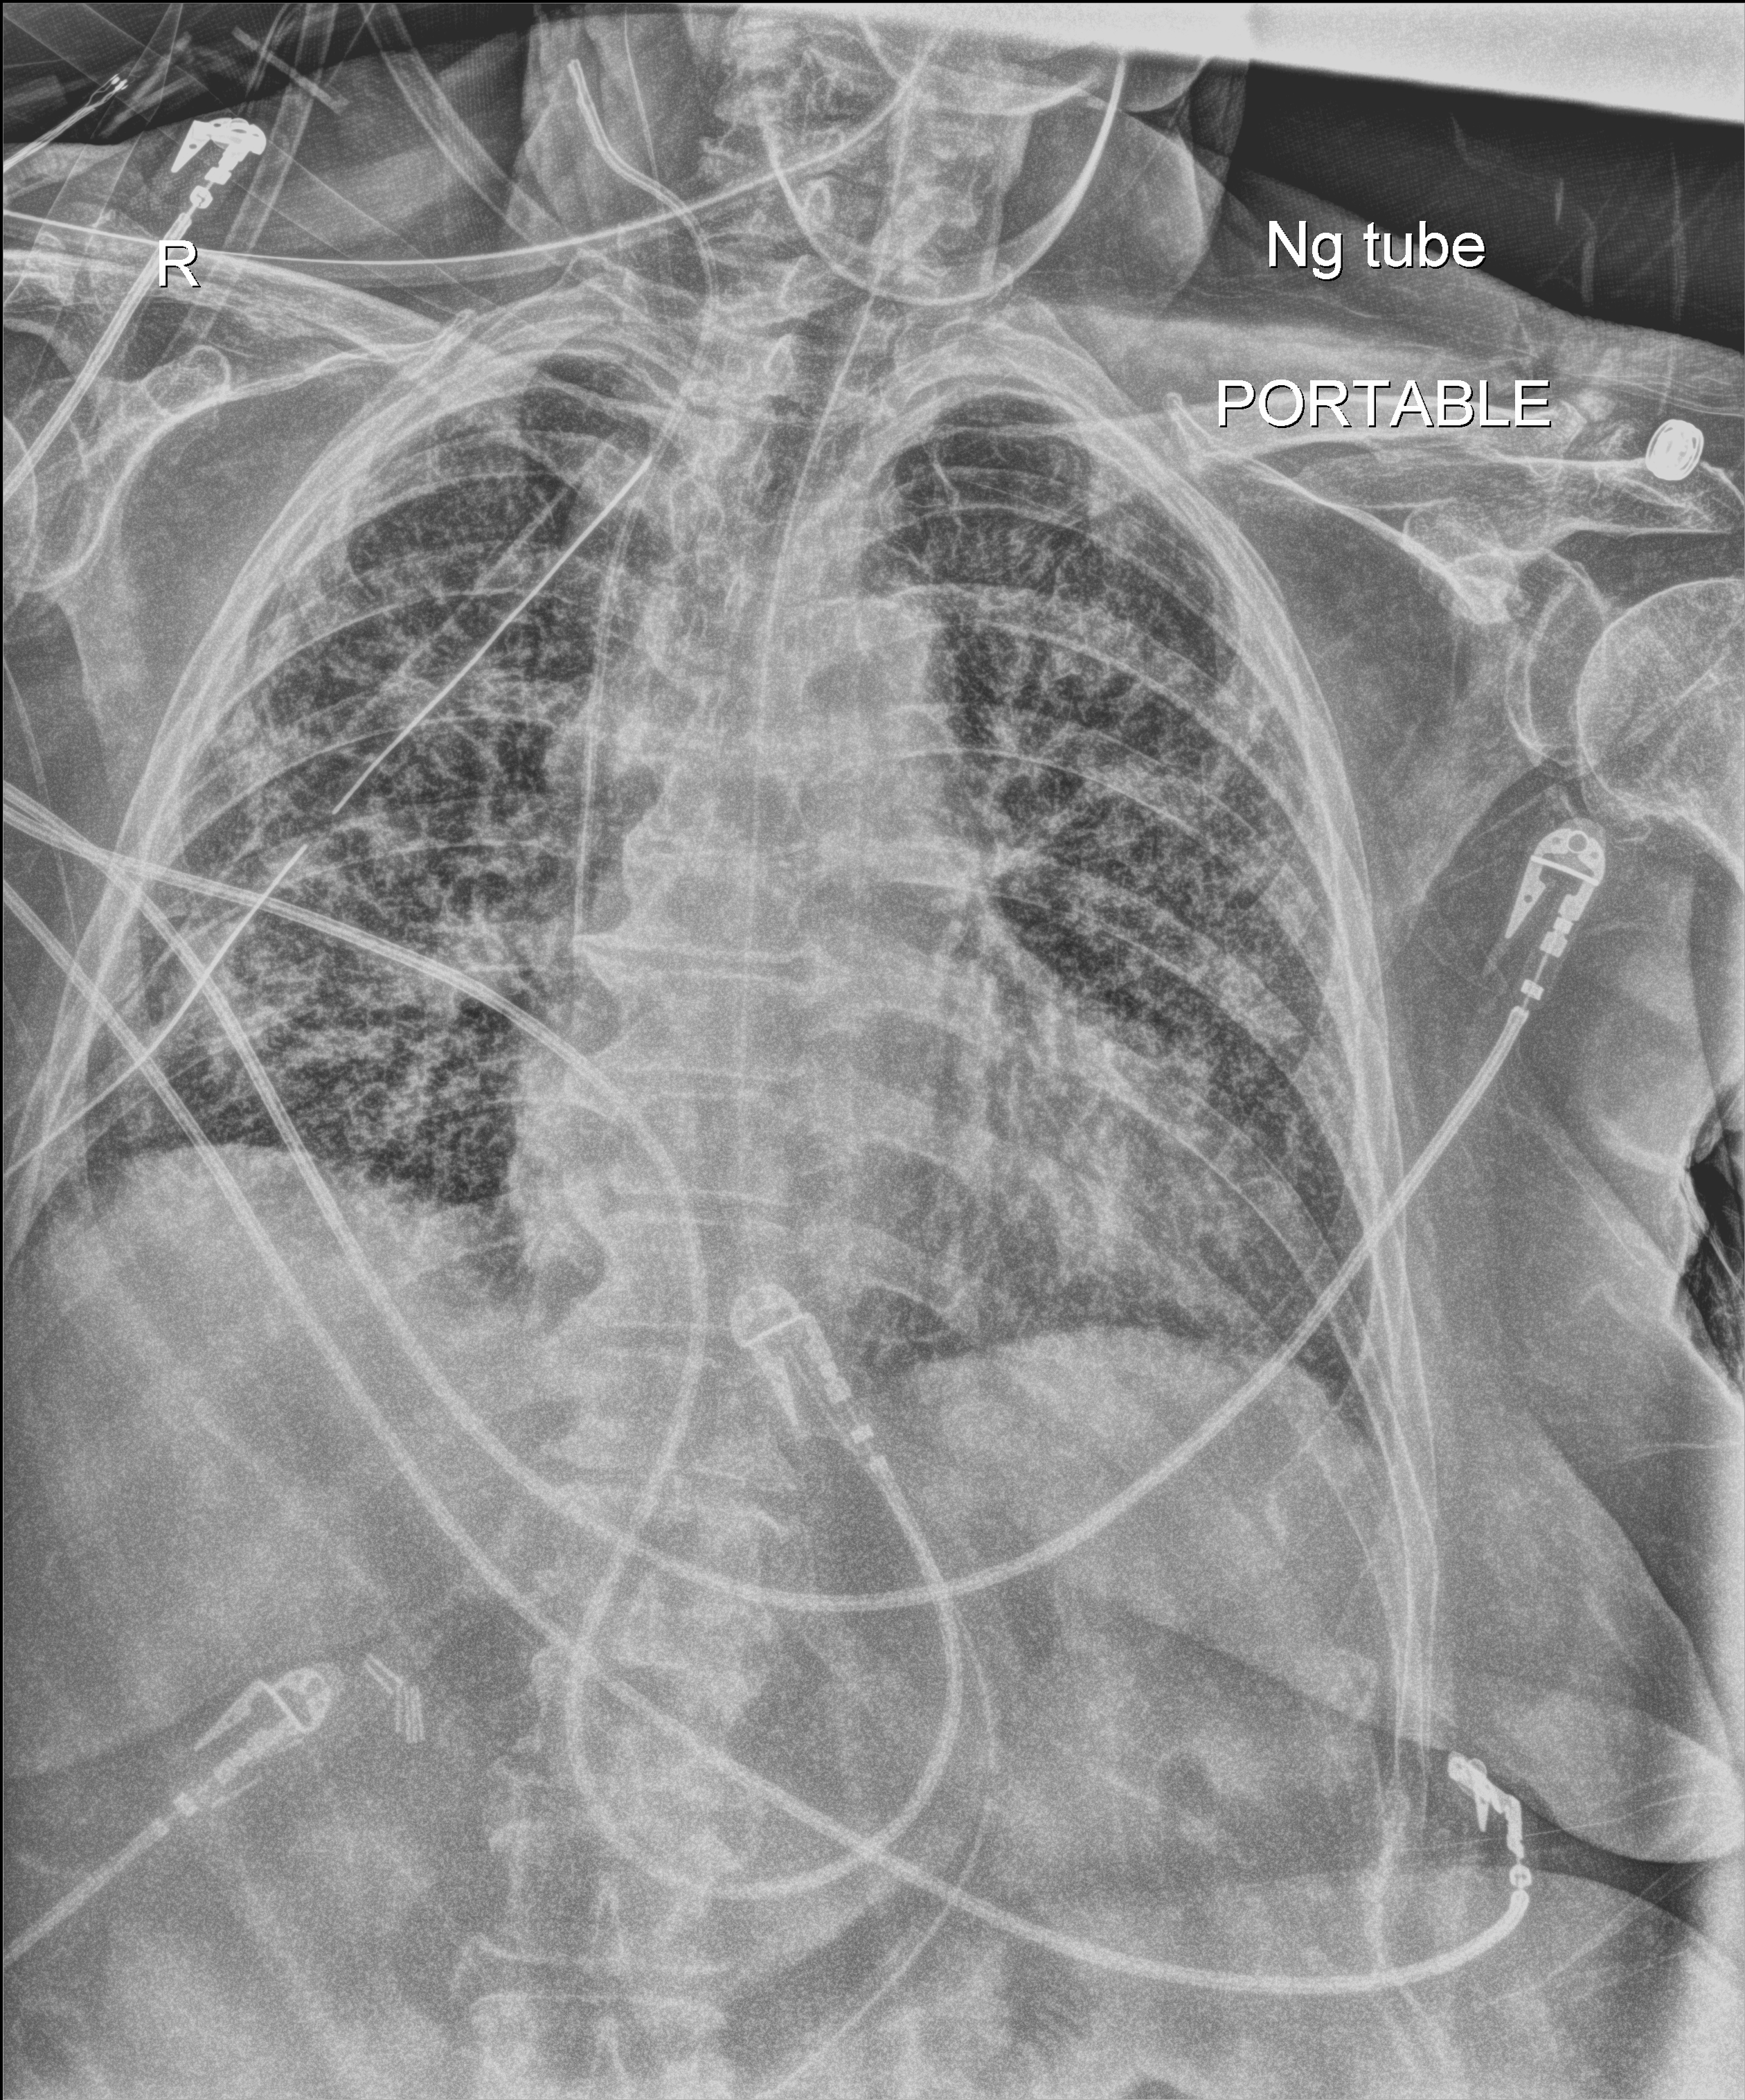
Portable chest radiograph, anteroposterior (AP) projection. Patient hospitalised with COVID-19; female, aged 75–90 years.
Hospital-stay facts (about this admission, not read from this image; timing relative to this image not recorded):
- admitted to intensive care during this hospital stay: no